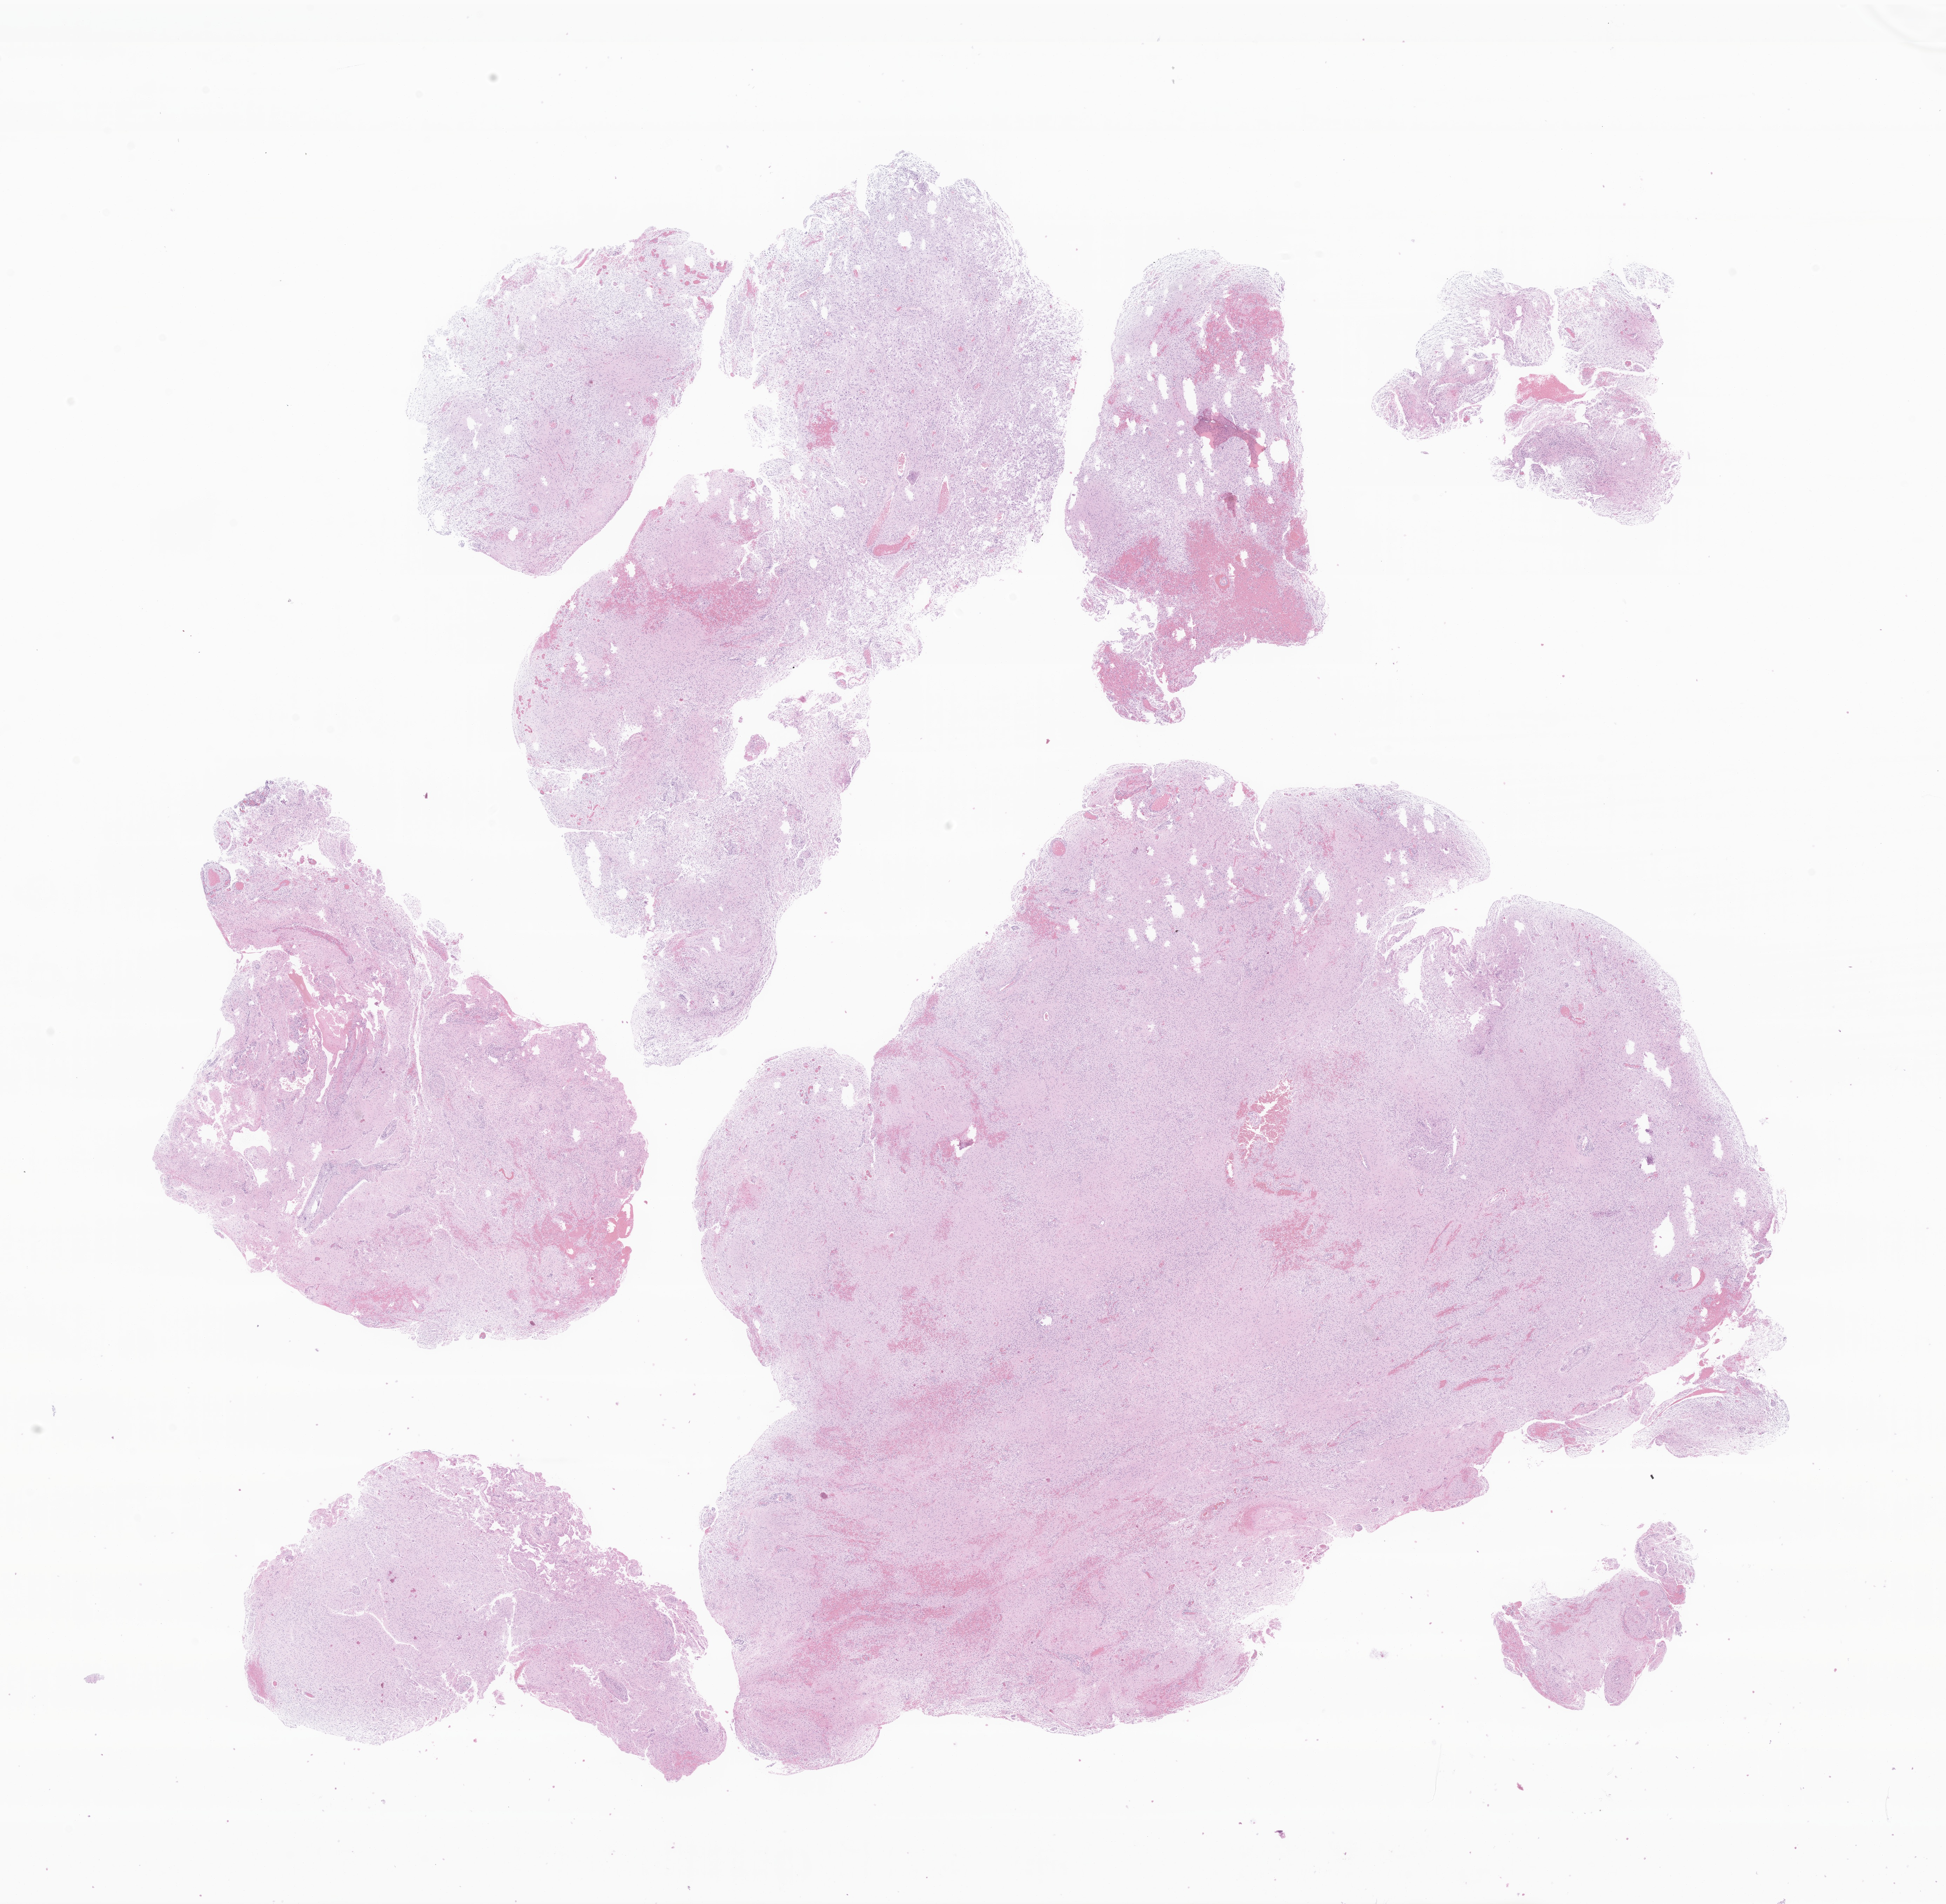
Digitized haematoxylin and eosin-stained section of tumor tissue from the brain — shown as a low-resolution overview of the whole scanned area (about 23.4 x 22.9 mm); FFPE section. Patient: male, age 138 months (11 years 6 months).
Recorded diagnosis: Pilocytic astrocytoma.